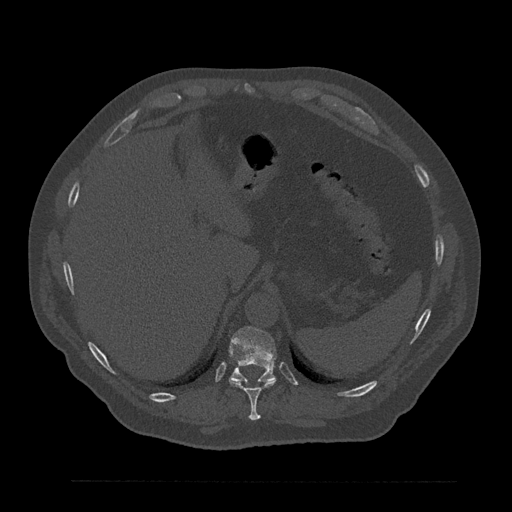
CT including the spine, one axial slice. Reconstruction kernel Br40s/3. 120 kVp. Bone window (W 1800 / L 400 HU). 0.5 mm slice thickness. 512 × 512 image matrix, field of view 430 × 430 mm. Patient: male, 61 years. Case-level facts recorded for this patient, not image findings: primary cancer: prostate.
Annotated regions visible in this slice (semi-automatic segmentation, software-assisted and operator-edited):
- T10 vertebra: bounding box <229,379,276,421> (left, top, right, bottom; pixels)
- T11 vertebra: <230,326,277,383>